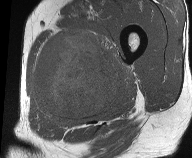
MRI of an extremity soft-tissue mass, one axial slice; MR volume resampled by the dataset authors to the PET/CT grid (not the native acquisition matrix); 192 × 158 image matrix, field of view 187 × 154 mm. Male patient. From the clinical record (not read from this slice): histological type: pleiomorphic liposarcoma; grade: high; site of the primary tumour: left thigh.
Structures marked on this image (expert contour drawn on MRI and transferred to this co-registered scan by the dataset authors):
- gross tumour volume including surrounding oedema: bounding box [x1, y1, x2, y2] px = [30, 28, 131, 125]
- gross tumour volume (mass): [34, 32, 117, 118]